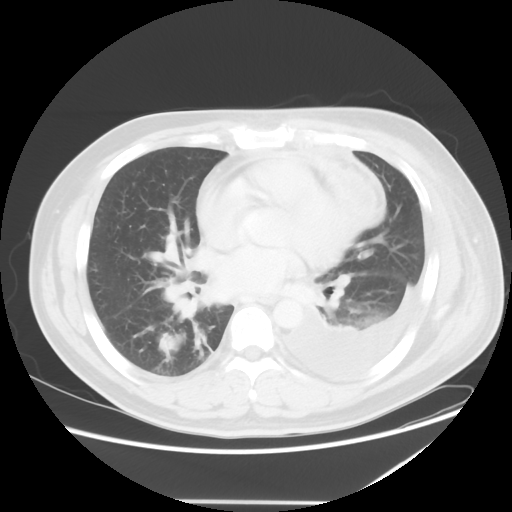
Chest CT, one axial slice. Slice 23 of 52 in the series (ordered by position). Reconstruction kernel STANDARD. 120 kVp. Lung window (W 1500 / L -600 HU). 512 × 512 image matrix, field of view 405 × 405 mm. Patient: male, 42 years. Case-level facts recorded for this patient, not image findings: clinical TNM (as recorded): T2 N1 M1.
Annotated regions visible in this slice (bounding box drawn by a radiologist):
- lung tumour (recorded histology: adenocarcinoma): bounding box [x1, y1, x2, y2] px = [154, 324, 183, 356]